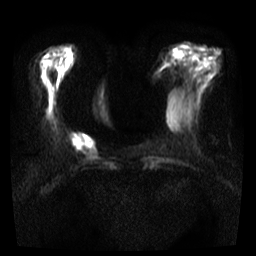
Breast MRI, one axial slice; position 11 of 35 along the scan axis; diffusion-weighted series; image 2 of 4 stored at this slice position (different b-values; order by instance number); 3 T; 256 × 256 image matrix. Female patient.
Outlined on this slice (expert manual segmentation):
- tumour on diffusion-weighted imaging: bounding box (x1, y1, x2, y2) in pixels: (68, 132, 95, 153)